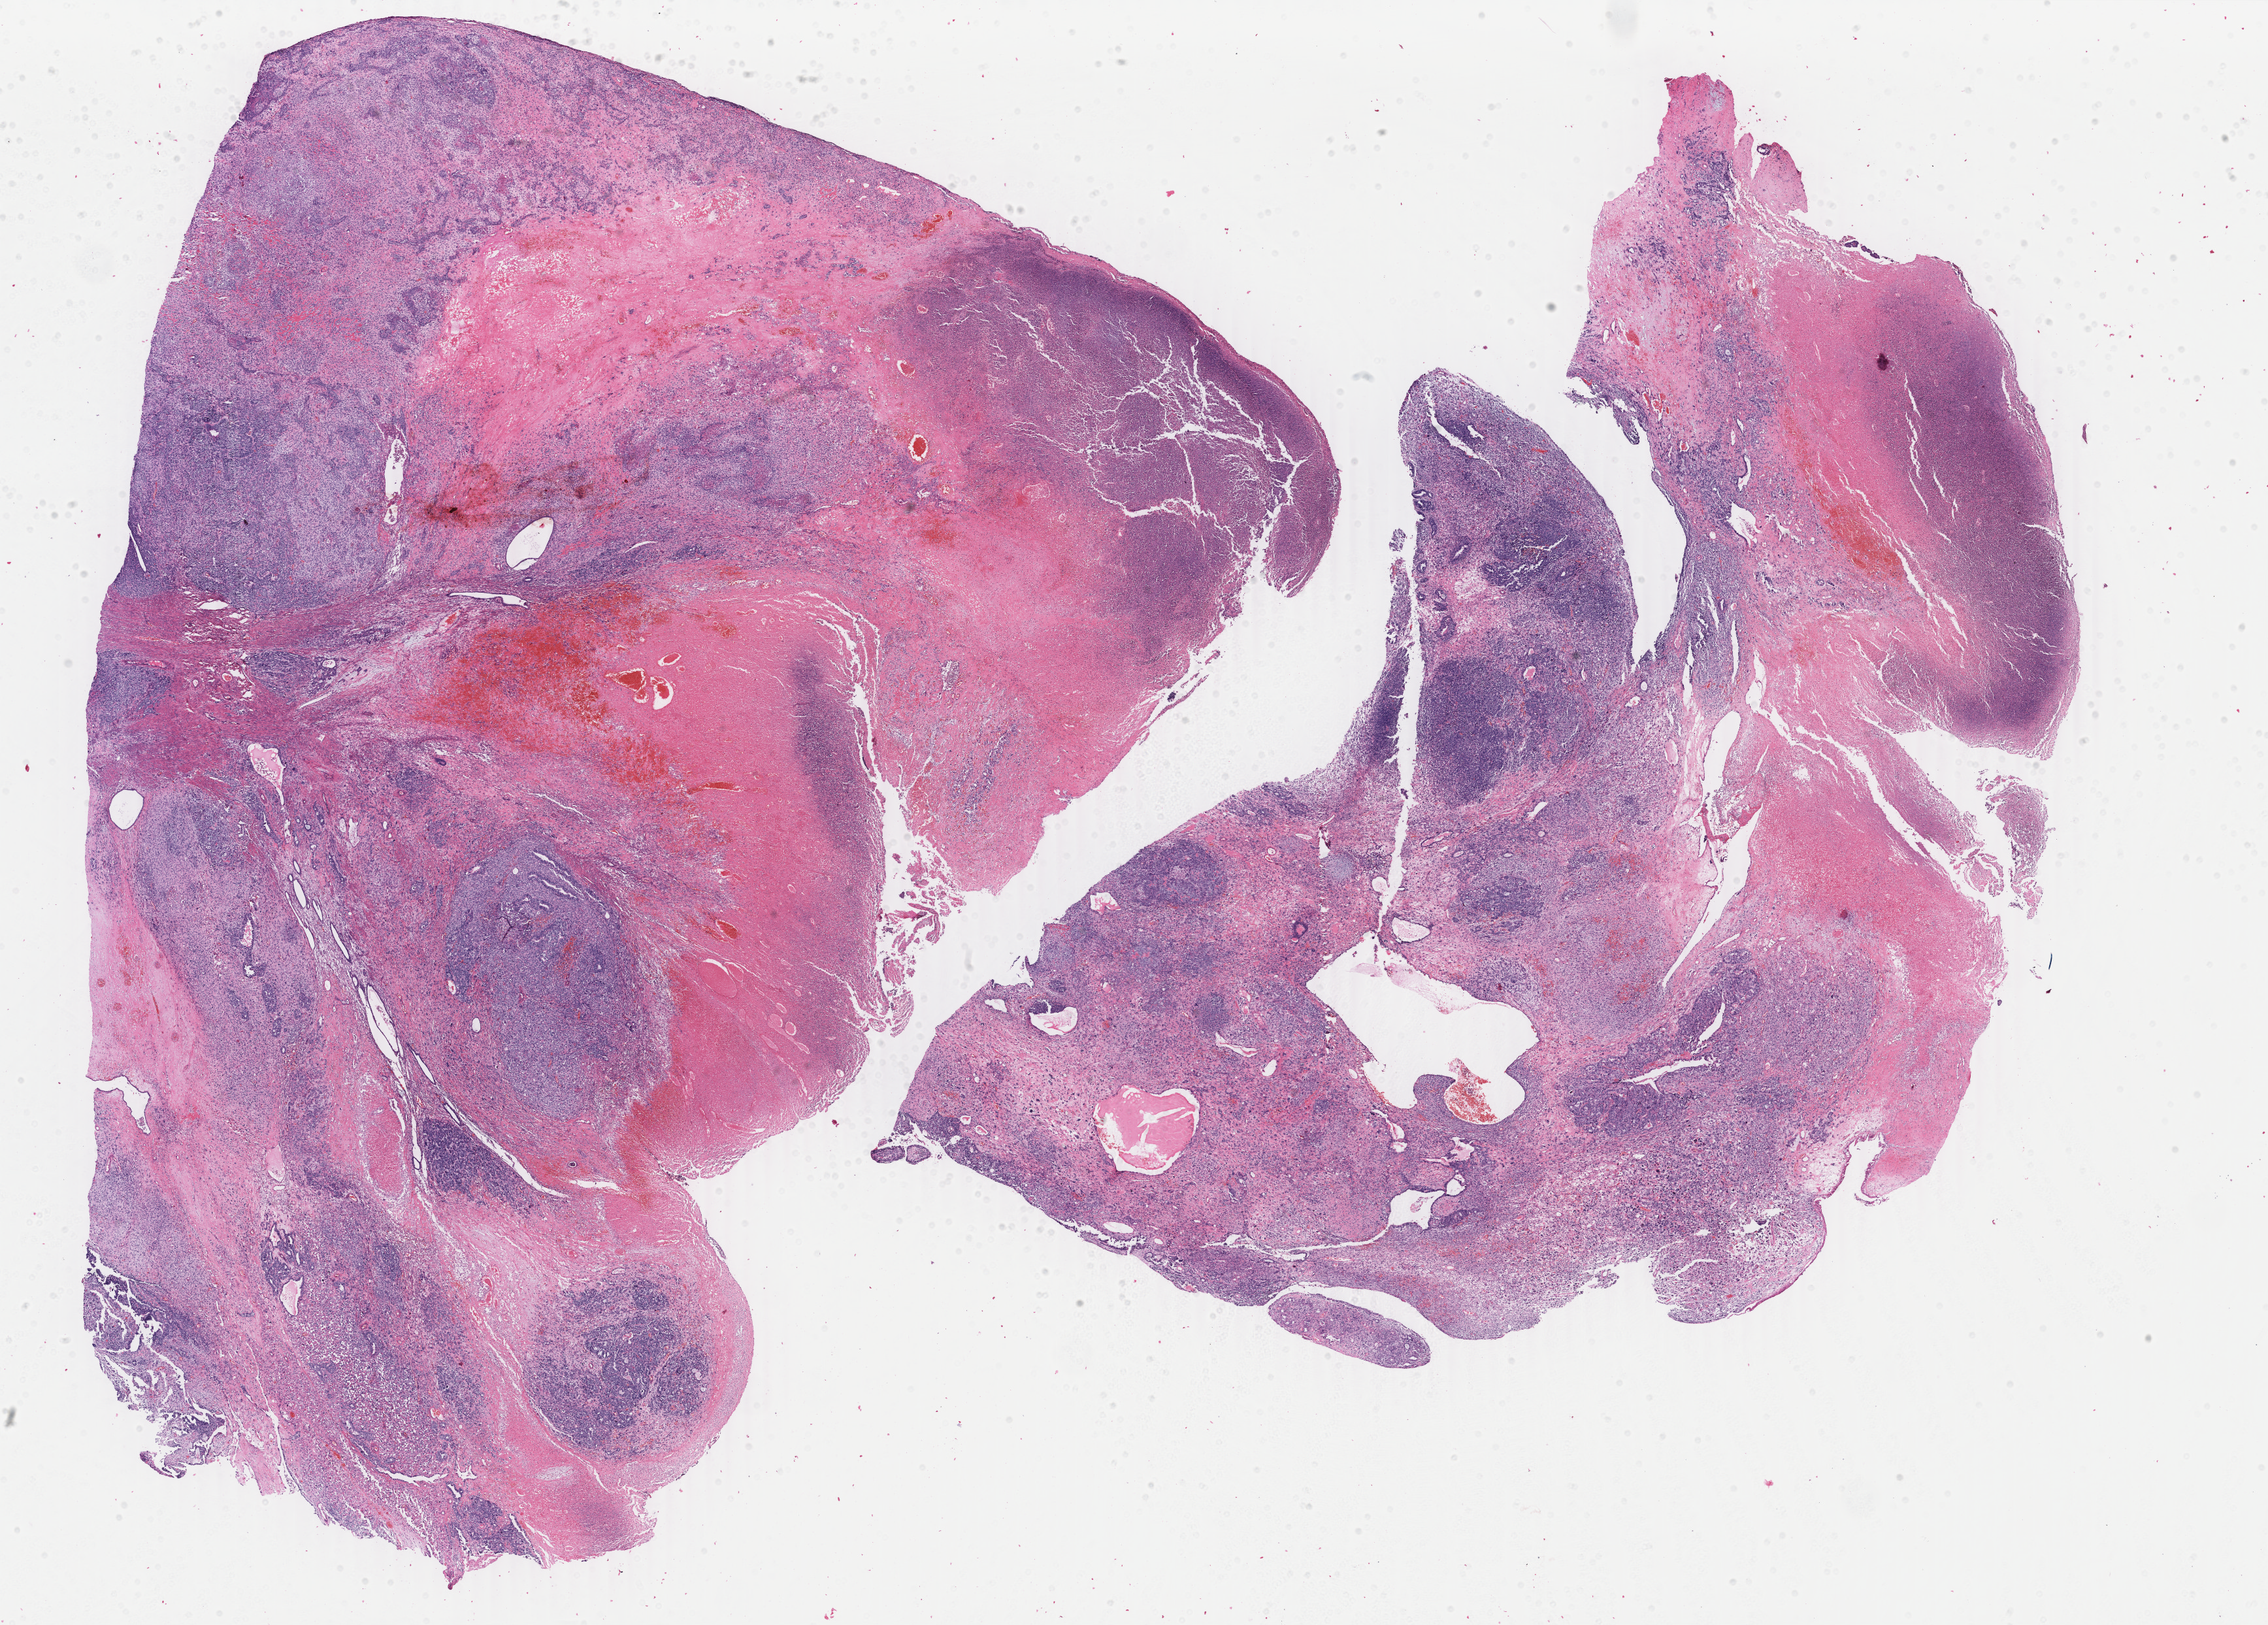
Digitized H&E tissue section (whole slide), a low-resolution overview of the entire scanned area, about 27.6 x 19.8 mm (from a 40x scan), formalin-fixed paraffin-embedded (FFPE) diagnostic section, primary tumour sample from the uterus. Female, age 72 years at initial diagnosis.
* pathologic diagnosis: Basal cell carcinoma, NOS (corpus uteri)
* FIGO stage: IB